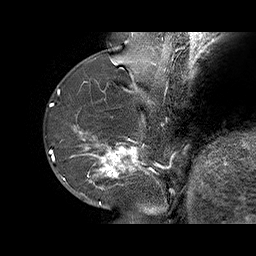
Breast MRI (dynamic contrast-enhanced), one sagittal slice; dynamic contrast-enhanced series, time point 2 of 6 at this slice position (early post-contrast); 1.5 T; TE 4.5 ms, TR 32.4 ms; 3 mm slice thickness; 256 × 256 image matrix, field of view 180 × 180 mm. Female patient. From the clinical record (not read from this slice): setting: breast cancer imaged before/during neoadjuvant chemotherapy; receptor status: HR-positive, HER2-negative.
Structures marked on this image (semi-automatically segmented with operator editing):
- analysis volume of interest (the breast-tissue region the enhancement analysis was run in; not a lesion): box from (x=71, y=128) to (x=159, y=202) px
- tumour enhancement mask (voxels above the 100 % enhancement threshold inside the analysis volume of interest): (x=72, y=128)–(x=149, y=189)